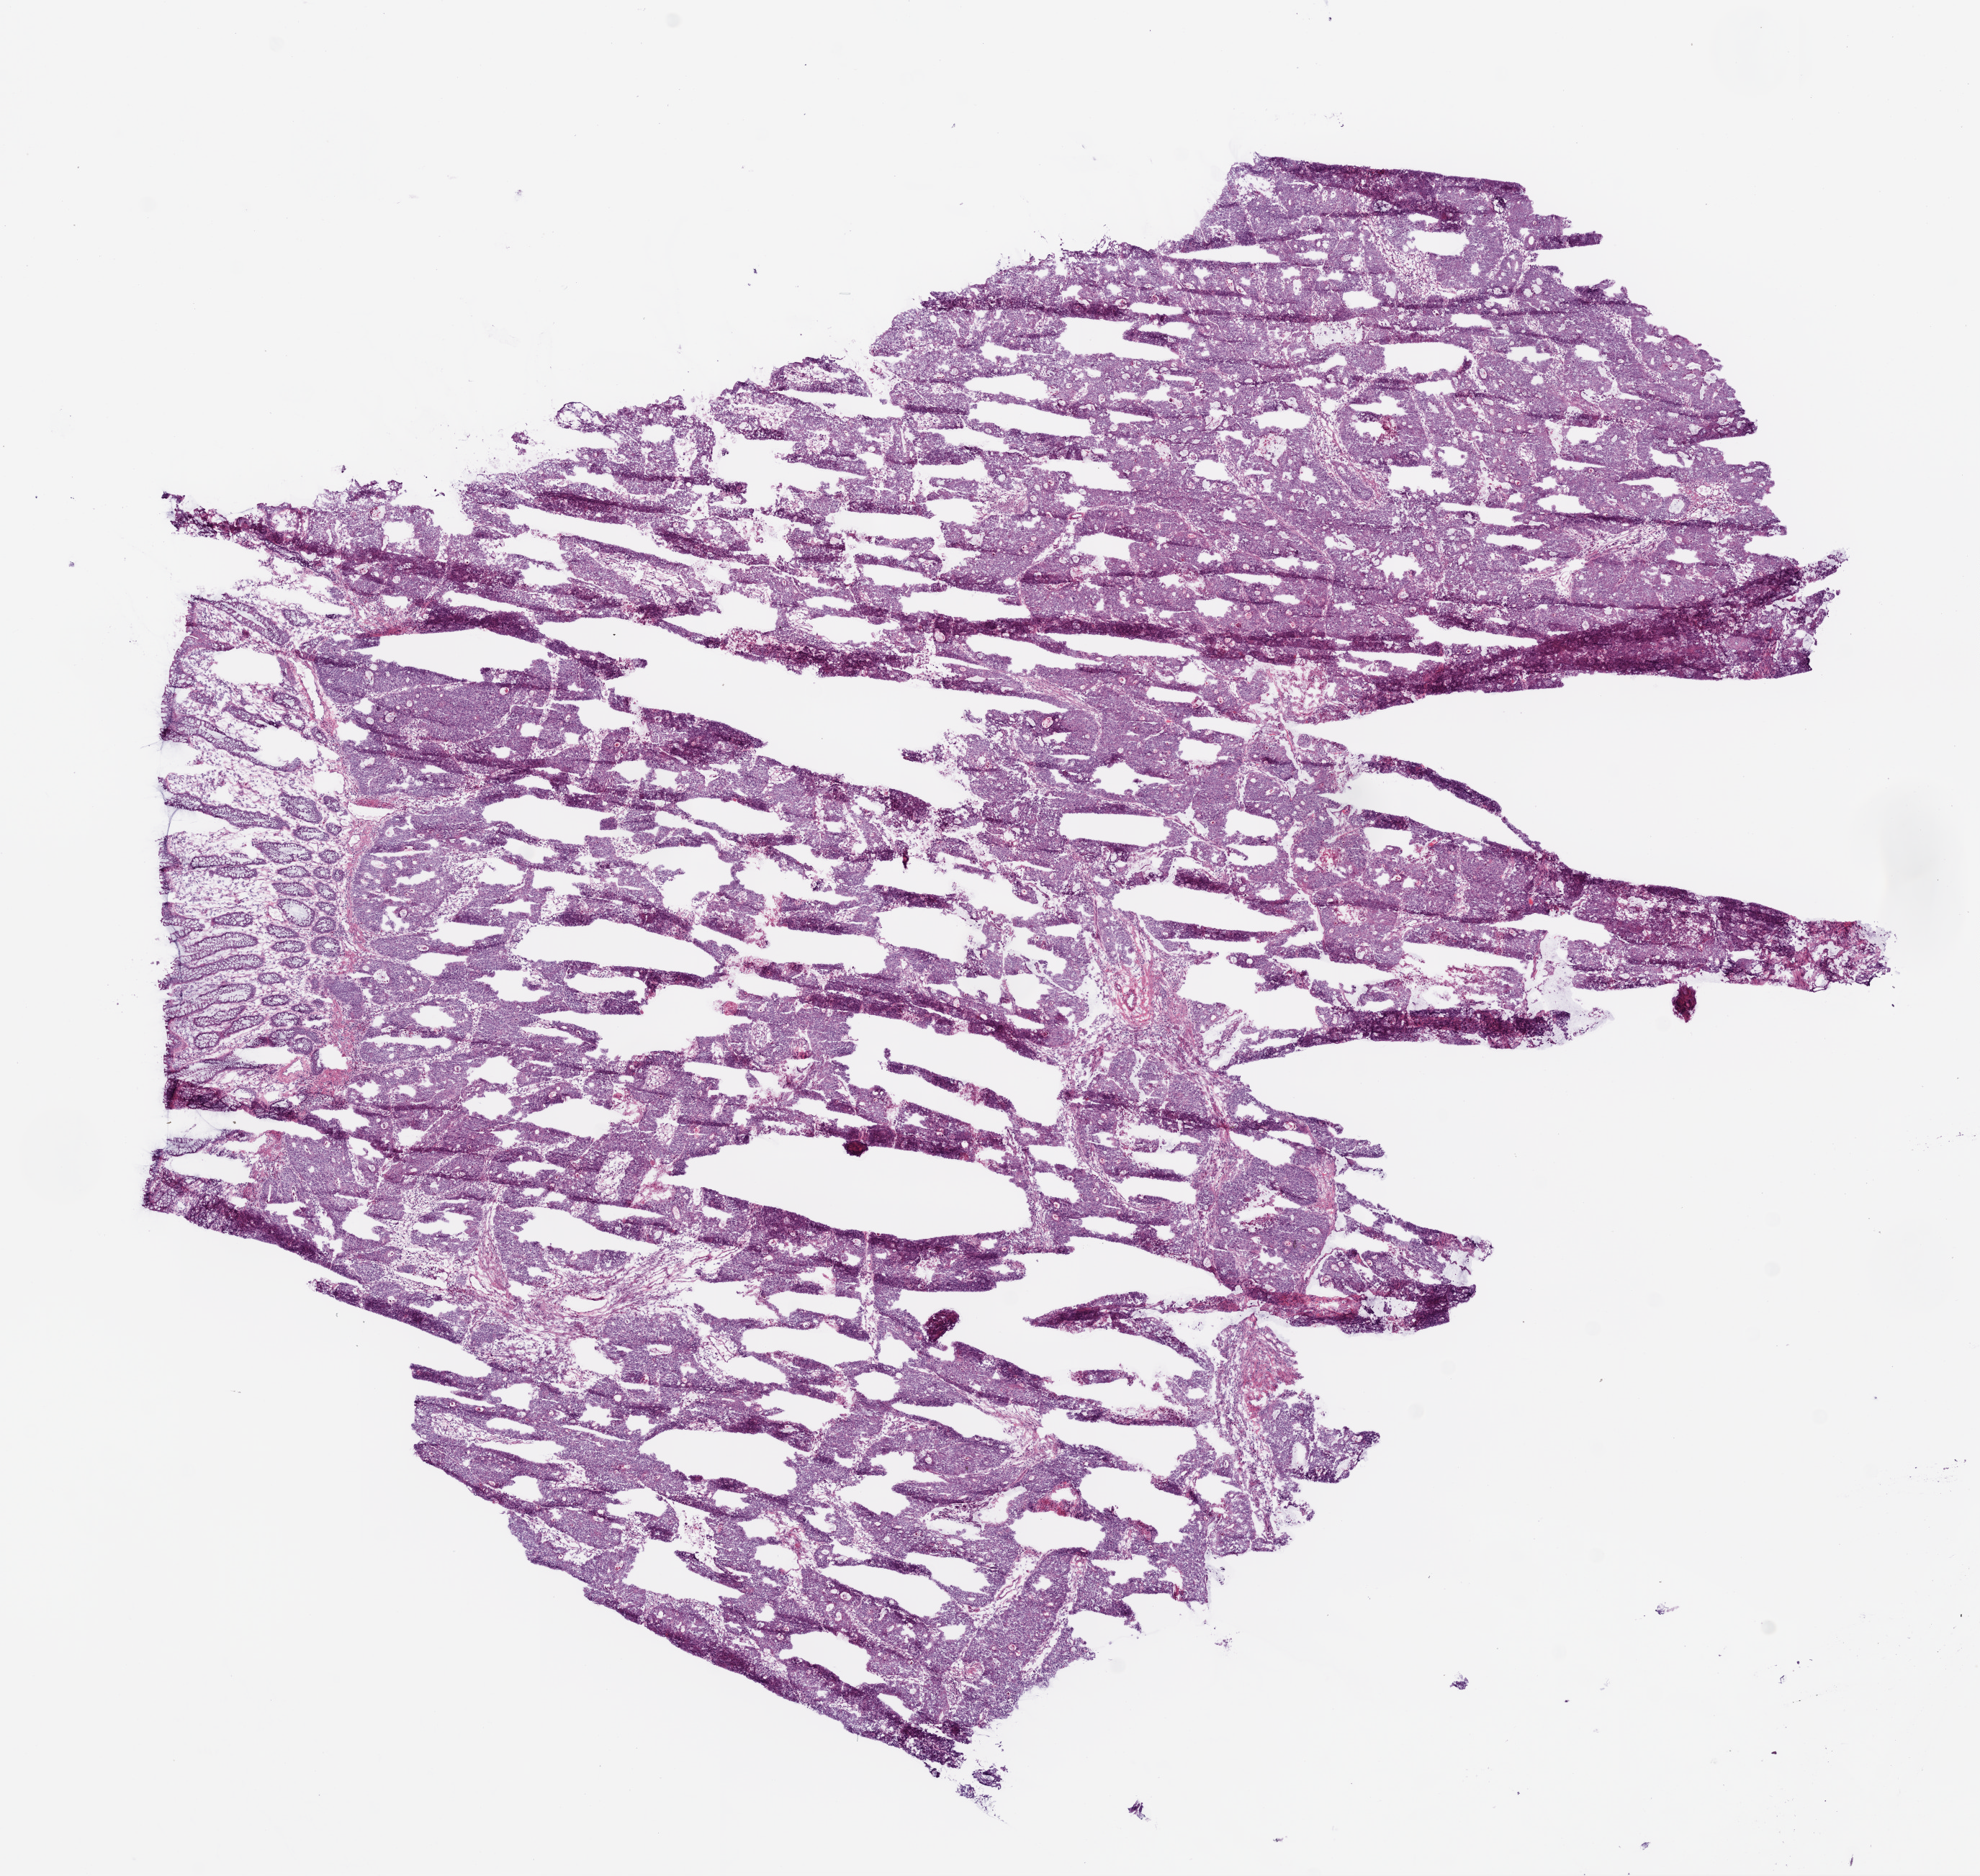
Whole-slide histology image, Hematoxylin and eosin (H&E) stained — whole scanned area (about 11.0 x 10.5 mm, acquisition: 20x scan) shown as a low-resolution overview. Frozen section. Primary tumour sample from the rectum. Female, age 72 years at initial diagnosis. Slide review estimates, as recorded: tumour cells 75%, tumour nuclei 70%, normal cells 10%, stromal cells 5%, necrosis 10%.
• histologic diagnosis: Mucinous adenocarcinoma (rectosigmoid junction)
• TNM: T3 N2 M0
• AJCC pathologic stage: III (5th edition)